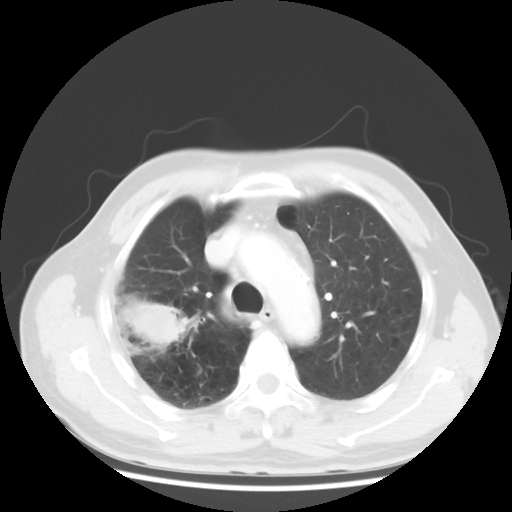
Chest CT, one axial slice; slice 37 of 50 in the series (ordered by position); reconstruction kernel STANDARD; lung window (W 1500 / L -600 HU); 512 × 512 image matrix, field of view 360 × 360 mm. Male patient, age 69 years. Case-level facts recorded for this patient, not image findings: clinical TNM (as recorded): T3 N0 M0.
Annotated regions visible in this slice (bounding box drawn by a radiologist):
- lung tumour (recorded histology: adenocarcinoma): box from (x=113, y=289) to (x=201, y=361) px